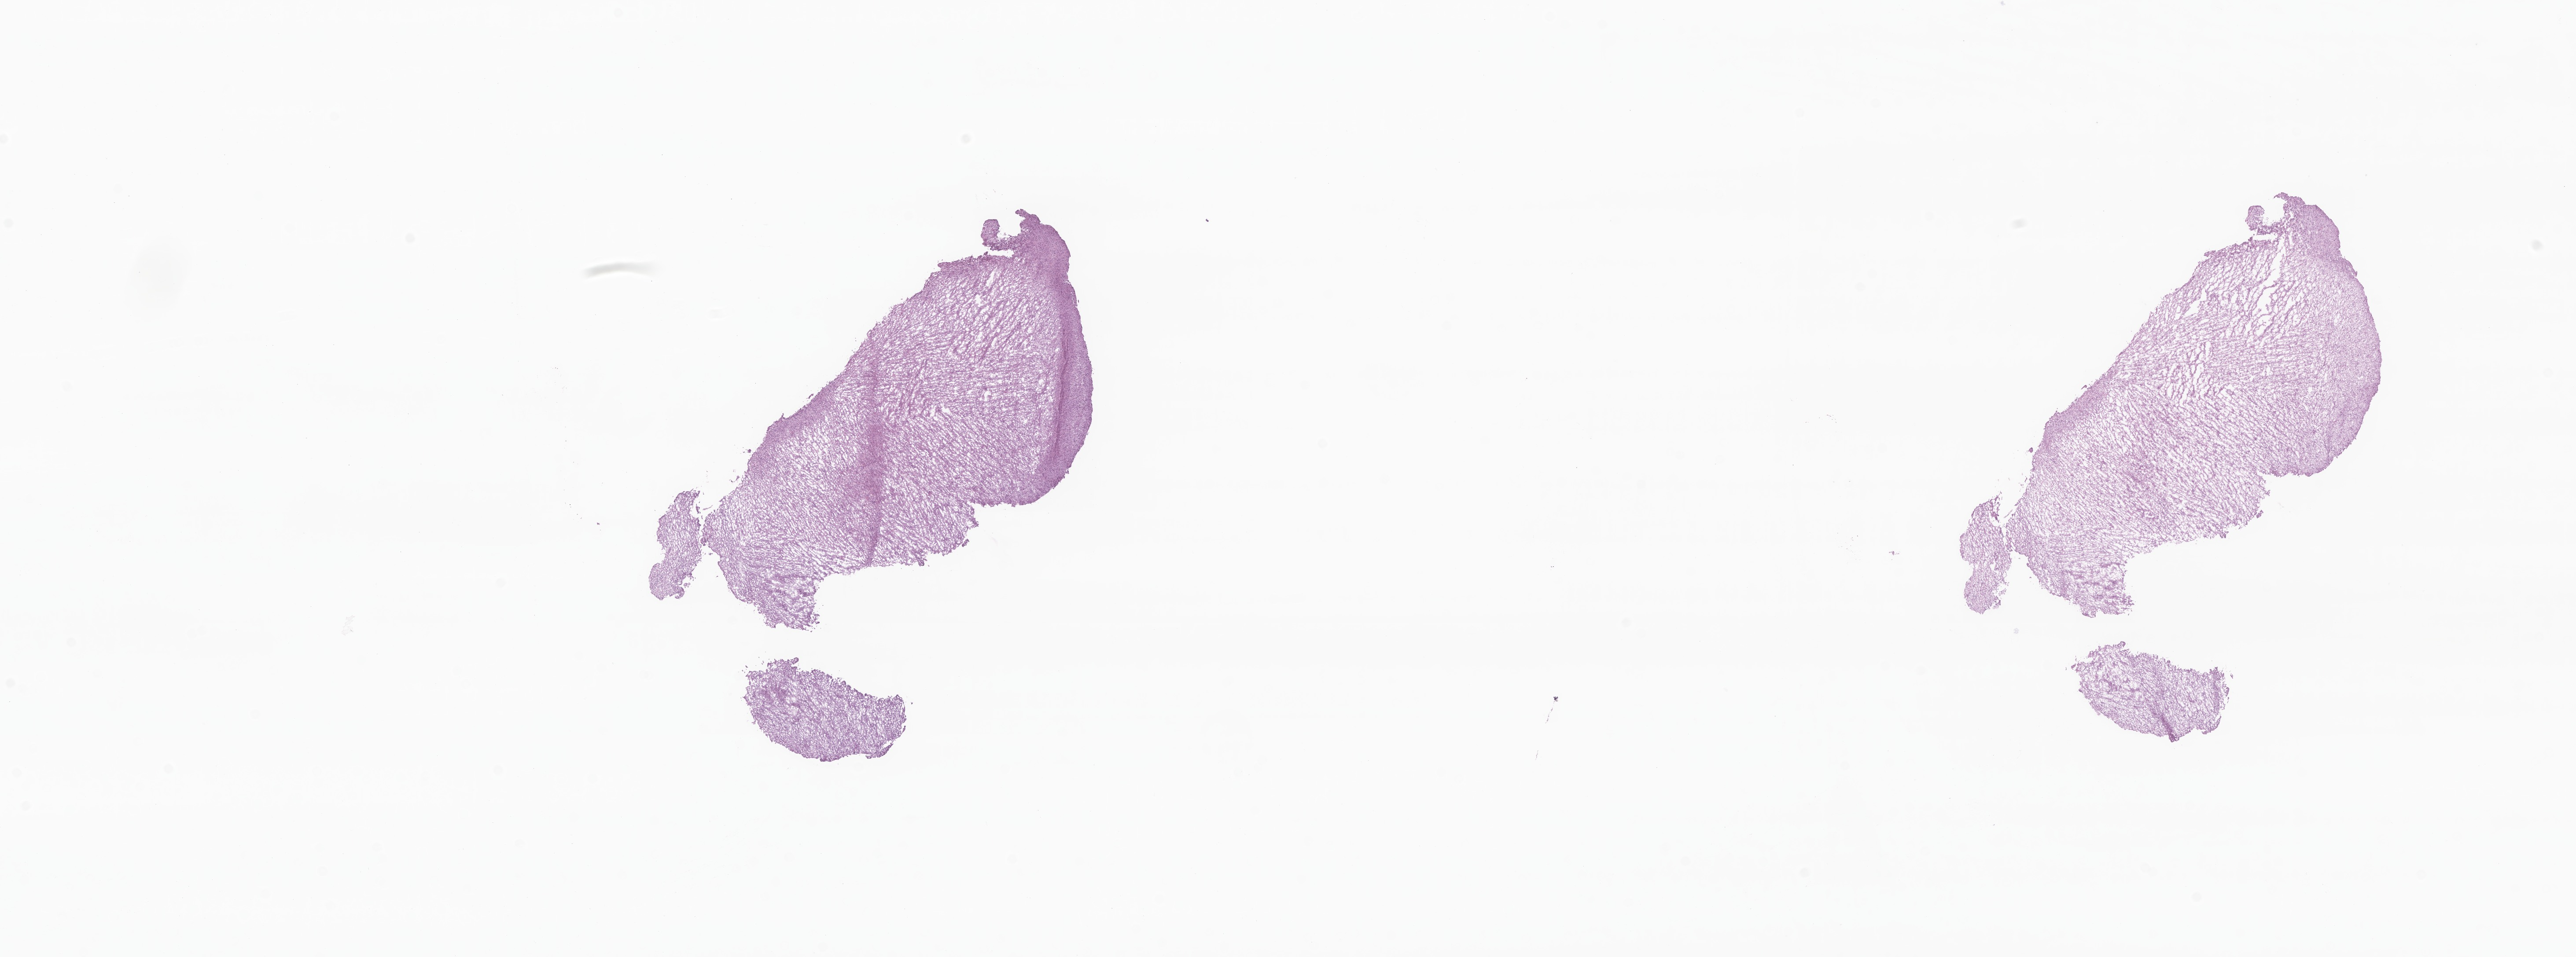
Hematoxylin and eosin (H&E) whole-slide image of tumor tissue from the temporal lobe — a low-resolution overview of the entire scanned area, about 24.7 x 9.2 mm, frozen section (OCT-embedded). Patient: female, age 54 months.
Diagnosis (ICD-O-3 morphology term): Glioma, malignant.